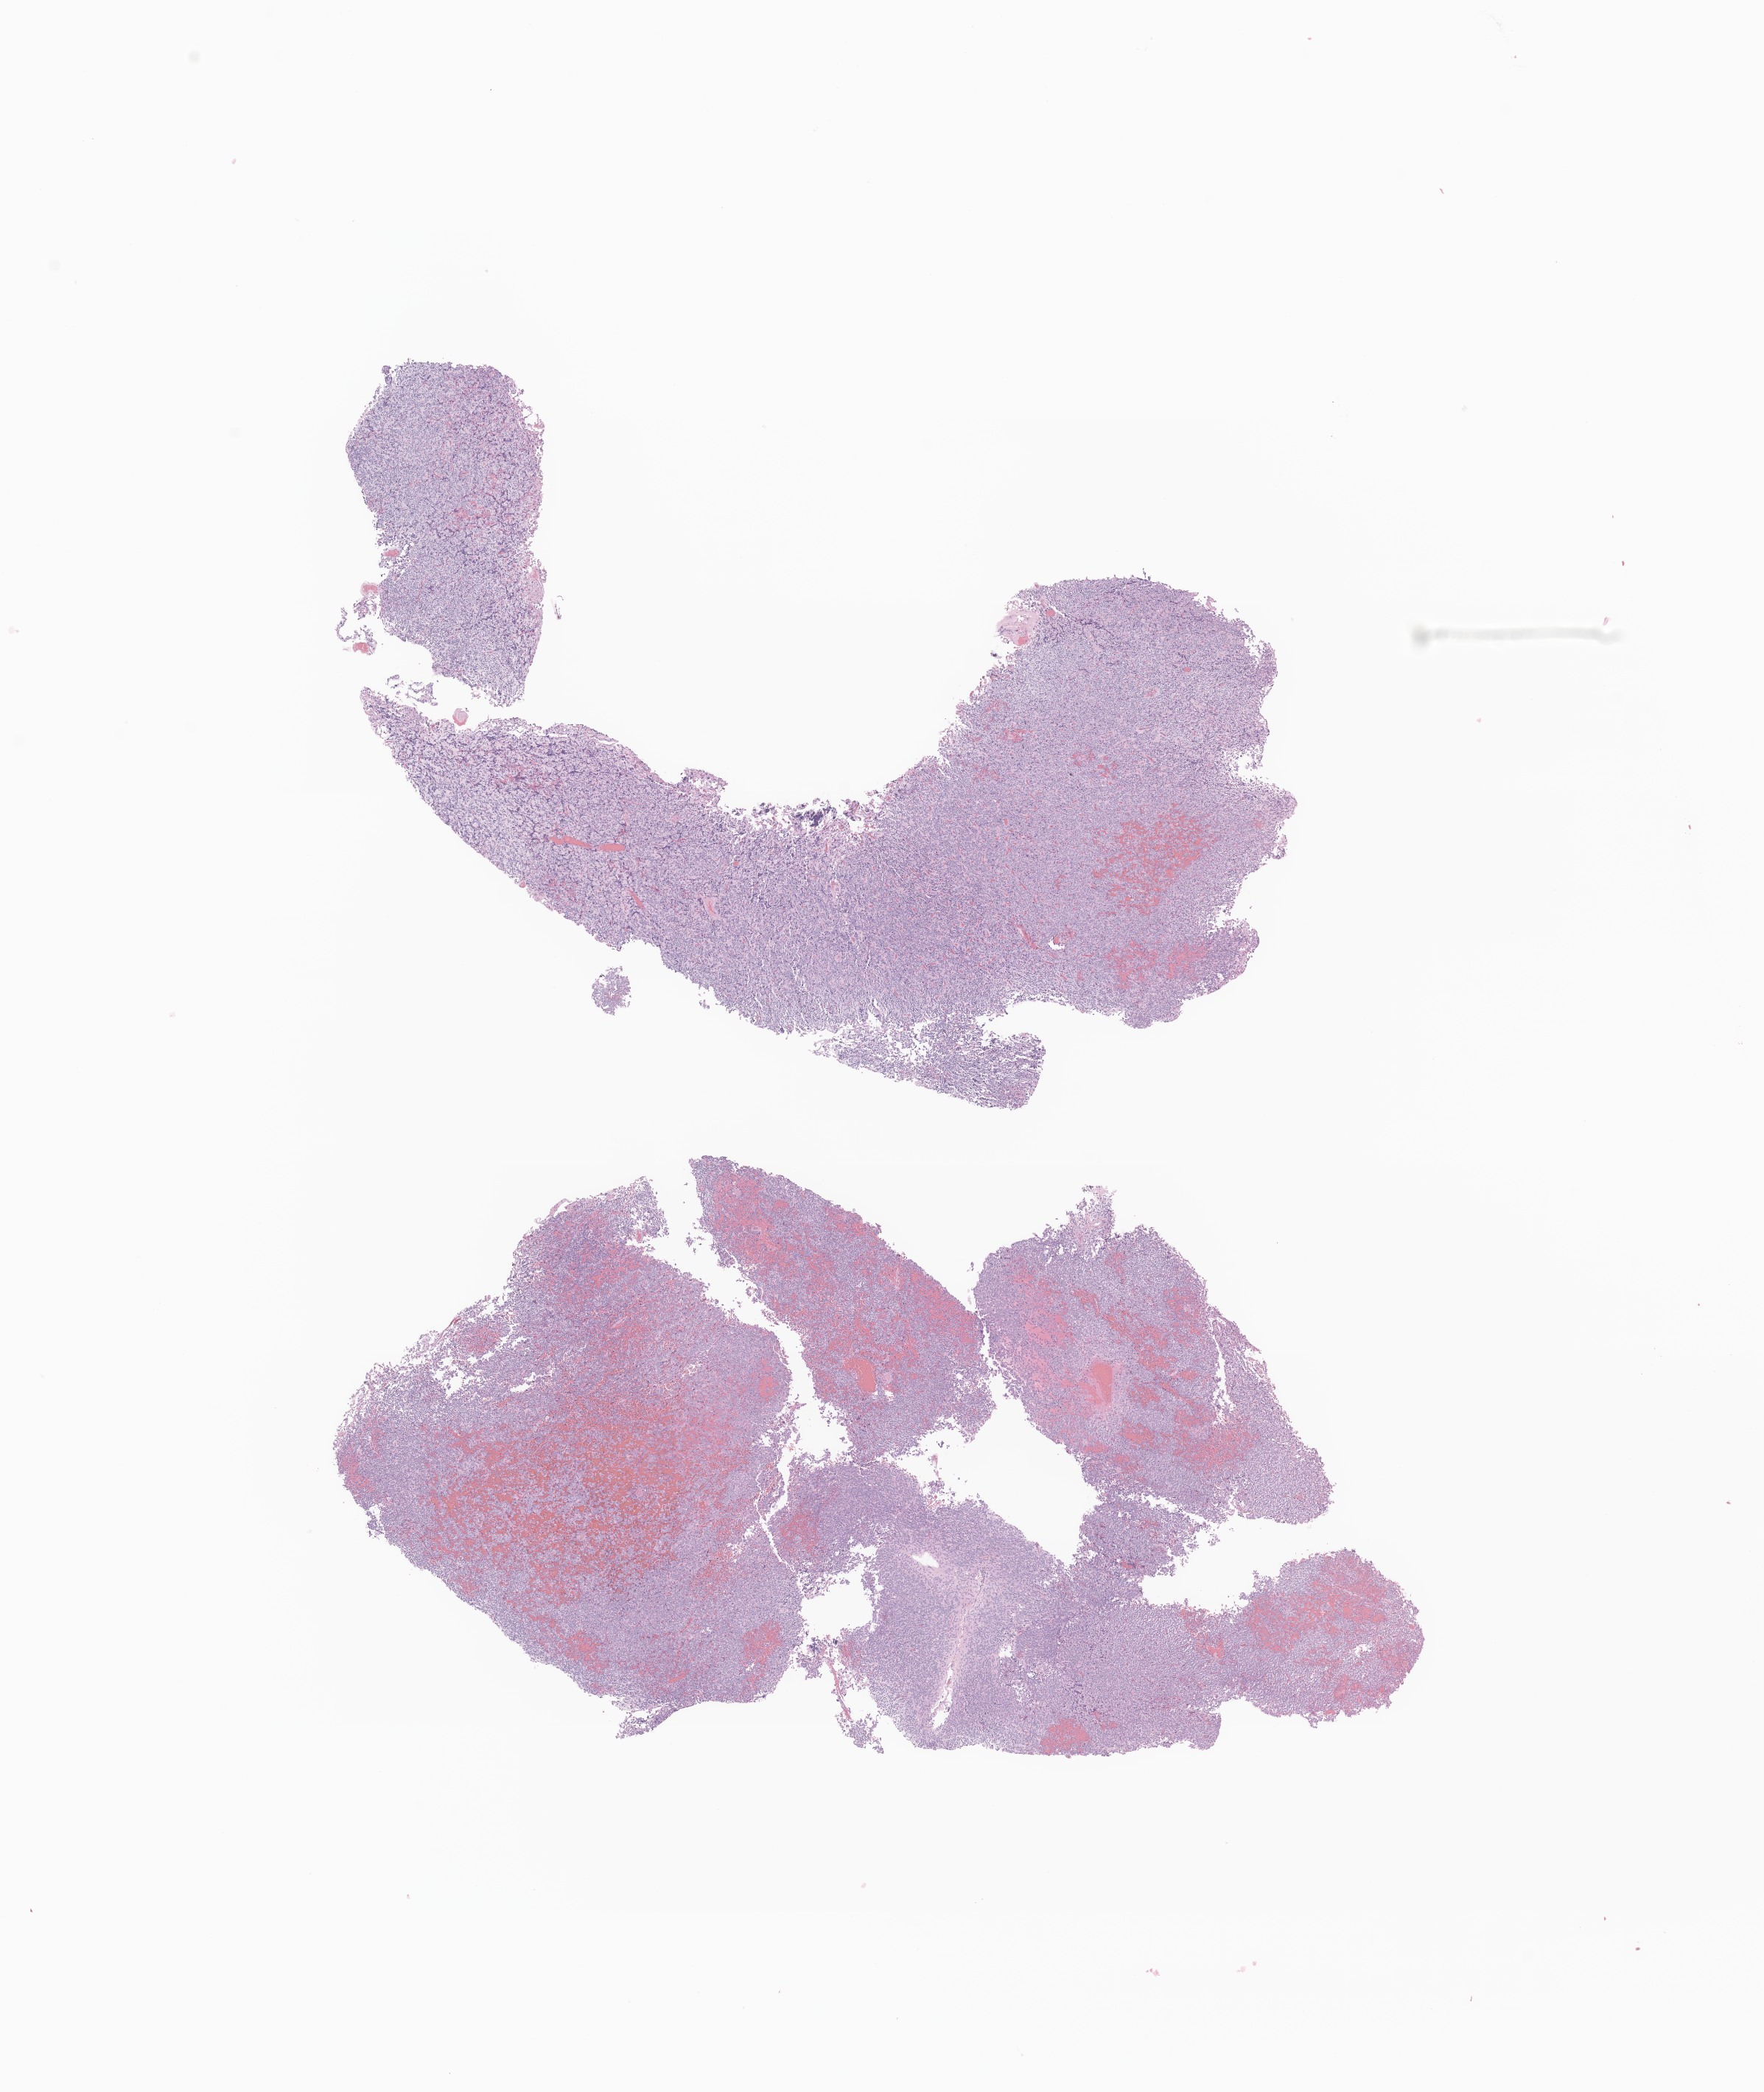
Whole-slide image, haematoxylin and eosin stain of tumor tissue from the cerebral ventricle, low-resolution overview of the scanned area, about 10.1 x 12.0 mm; FFPE section. Patient: male, age 229 months (19 years 1 month).
Diagnosis (ICD-O-3 morphology term): Central neurocytoma.